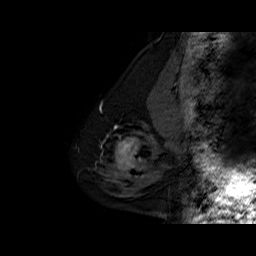
Breast MRI (dynamic contrast-enhanced), one sagittal slice. Dynamic contrast-enhanced series, time point 2 of 6 at this slice position (early post-contrast). 1.5 T. TE 6.3 ms, TR 32.5 ms. 256 × 256 image matrix, field of view 200 × 200 mm. Female patient. Case-level facts recorded for this patient, not image findings: setting: breast cancer imaged before/during neoadjuvant chemotherapy; receptor status: triple-negative.
Structures marked on this image (semi-automatically segmented with operator editing):
- analysis volume of interest (the breast-tissue region the enhancement analysis was run in; not a lesion): bounding box (x1, y1, x2, y2) in pixels: (102, 127, 162, 186)
- tumour enhancement mask (voxels above the 100 % enhancement threshold inside the analysis volume of interest): (115, 137, 156, 170)